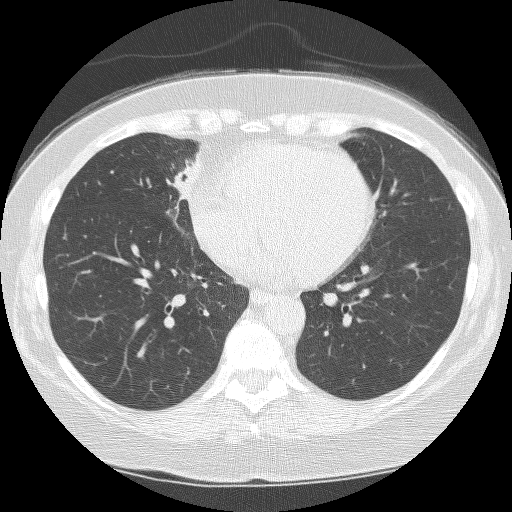
Low-dose screening chest CT, one axial slice. 120 kVp. Lung window (W 1500 / L -600 HU). 2.5 mm slice thickness. 512 × 512 image matrix, field of view 299 × 299 mm.
Outlined on this slice (outlined manually by an expert reader):
- lesion 1 (tumor, hilum of right lung): bounding box [x1, y1, x2, y2] px = [168, 154, 199, 201]